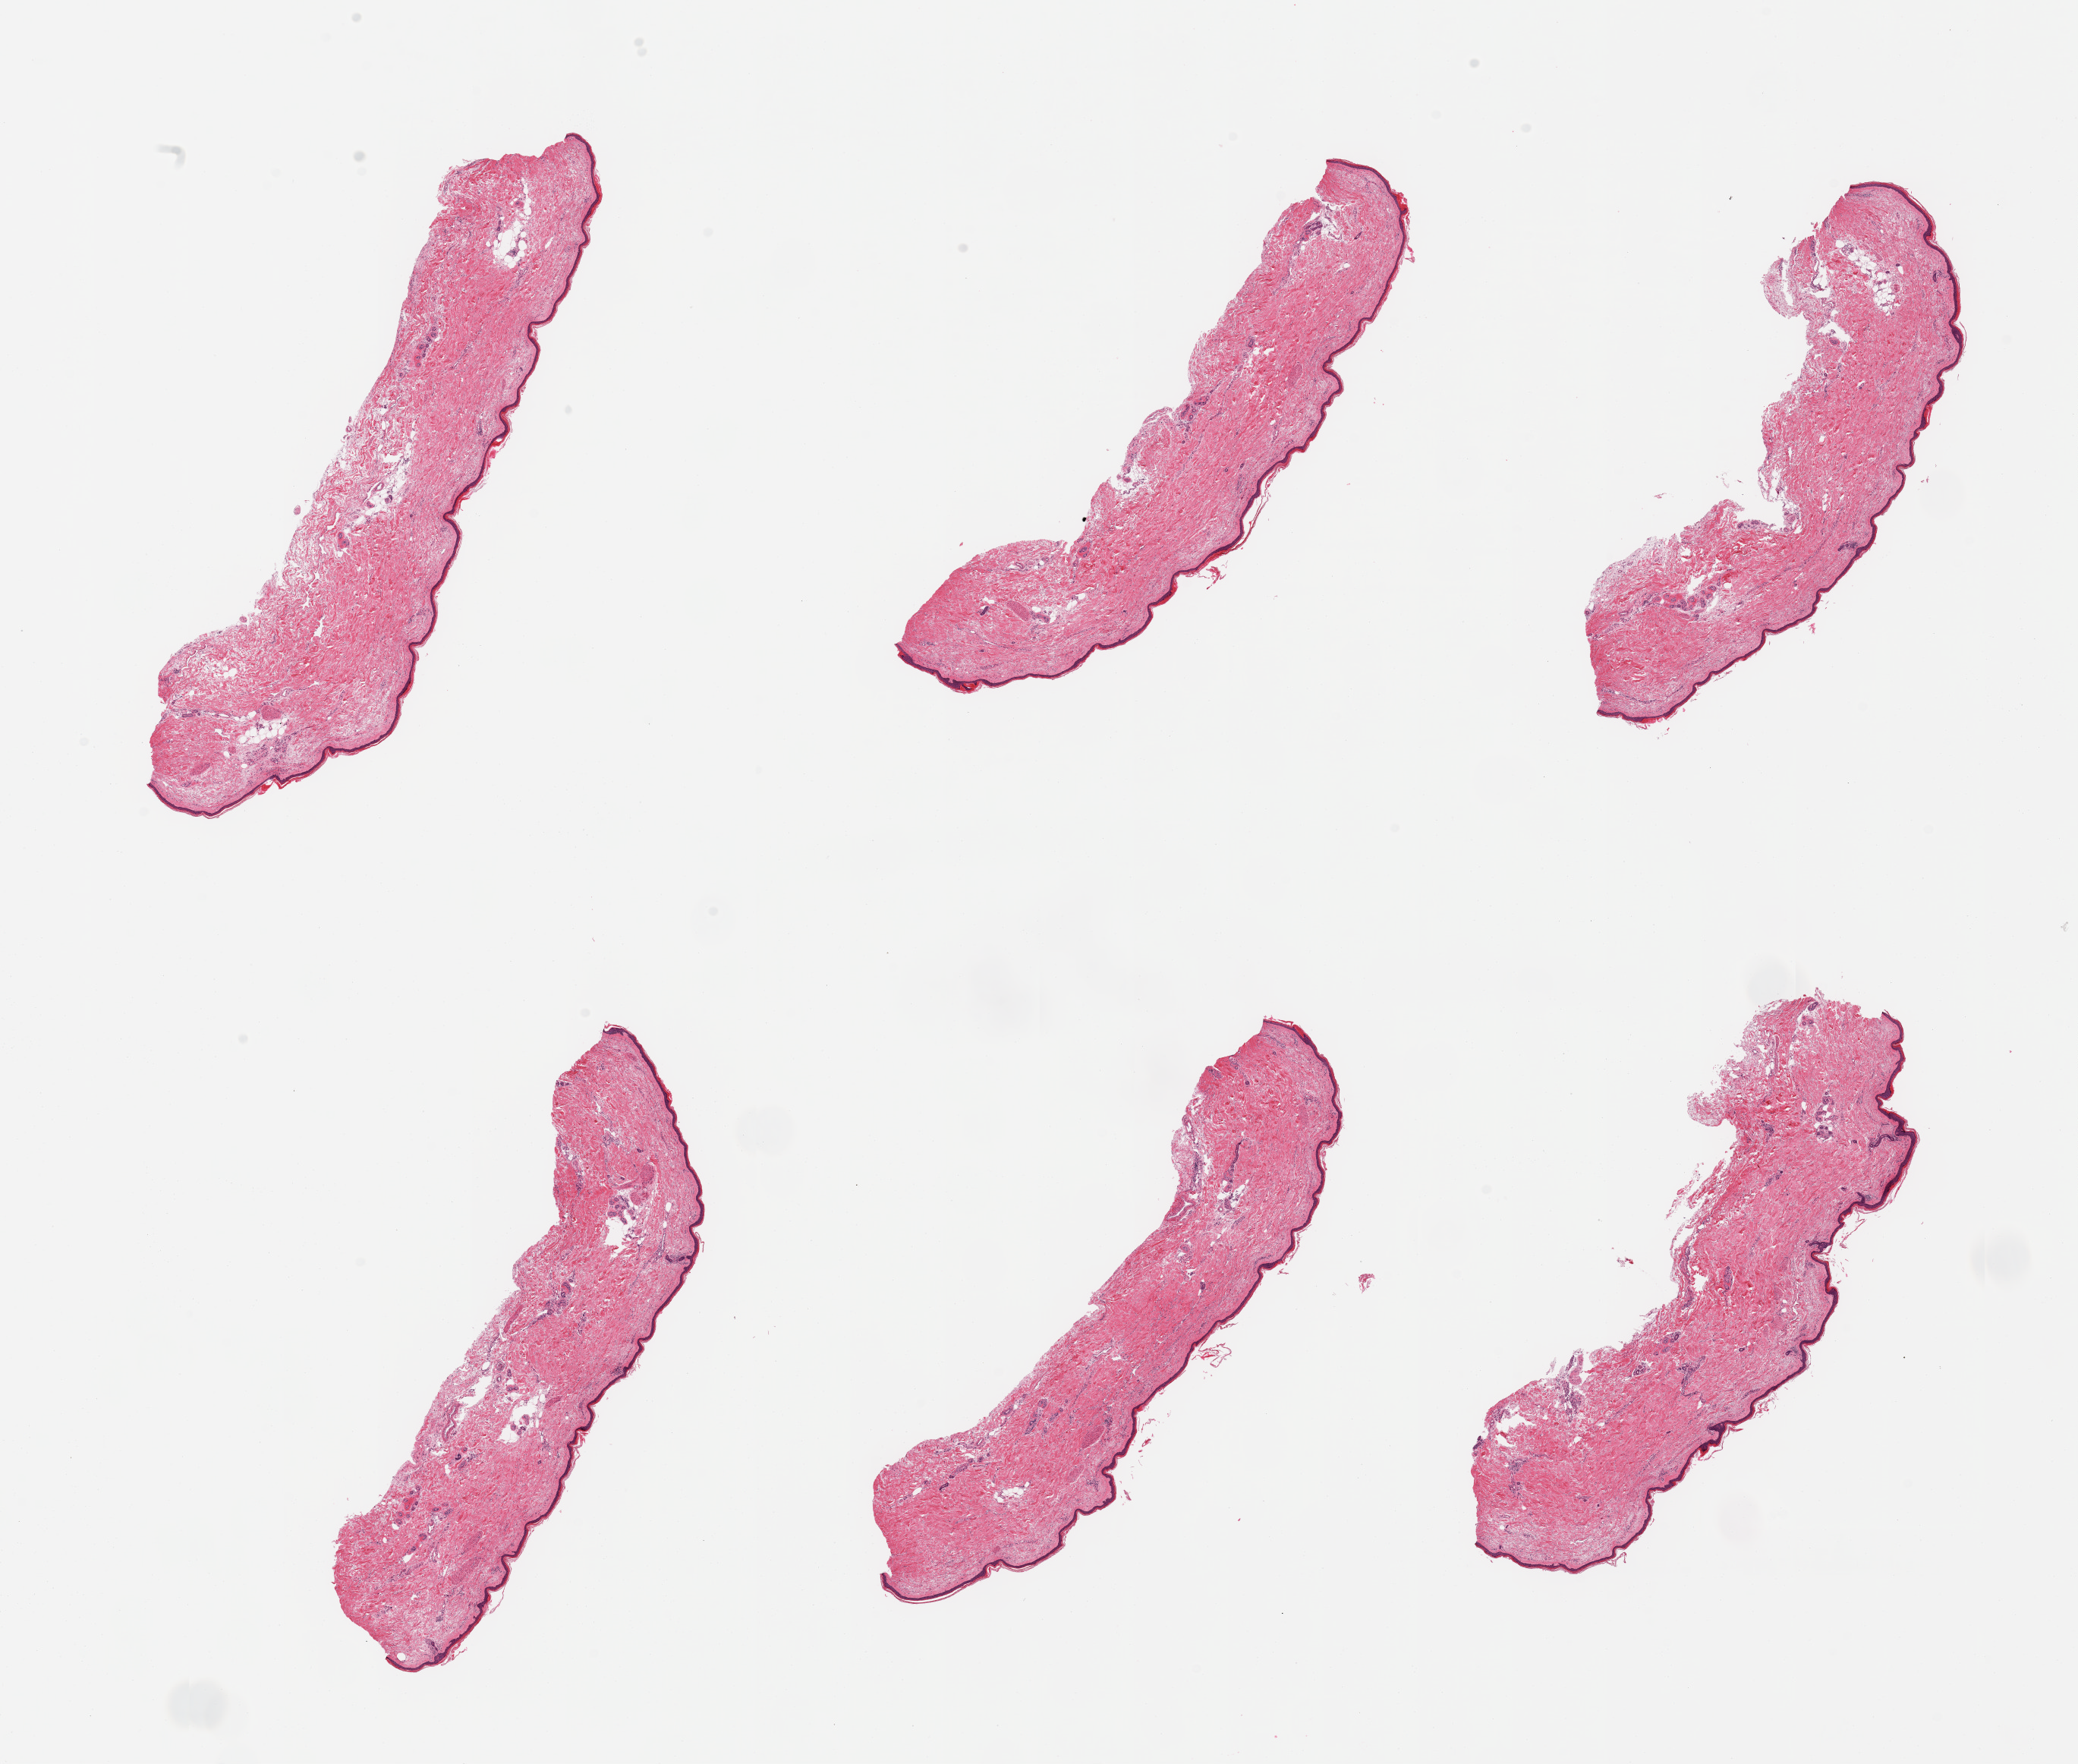
Whole-slide image, H&E stain — whole scanned area (about 21.7 x 18.4 mm) shown as a low-resolution overview. PAXgene-fixed paraffin-embedded (PFPE) section. Target tissue: skin of lower leg. Donor tissue sample.
Review note (as recorded): 6 pieces; well trimmed, epidermis measures 33 microns.